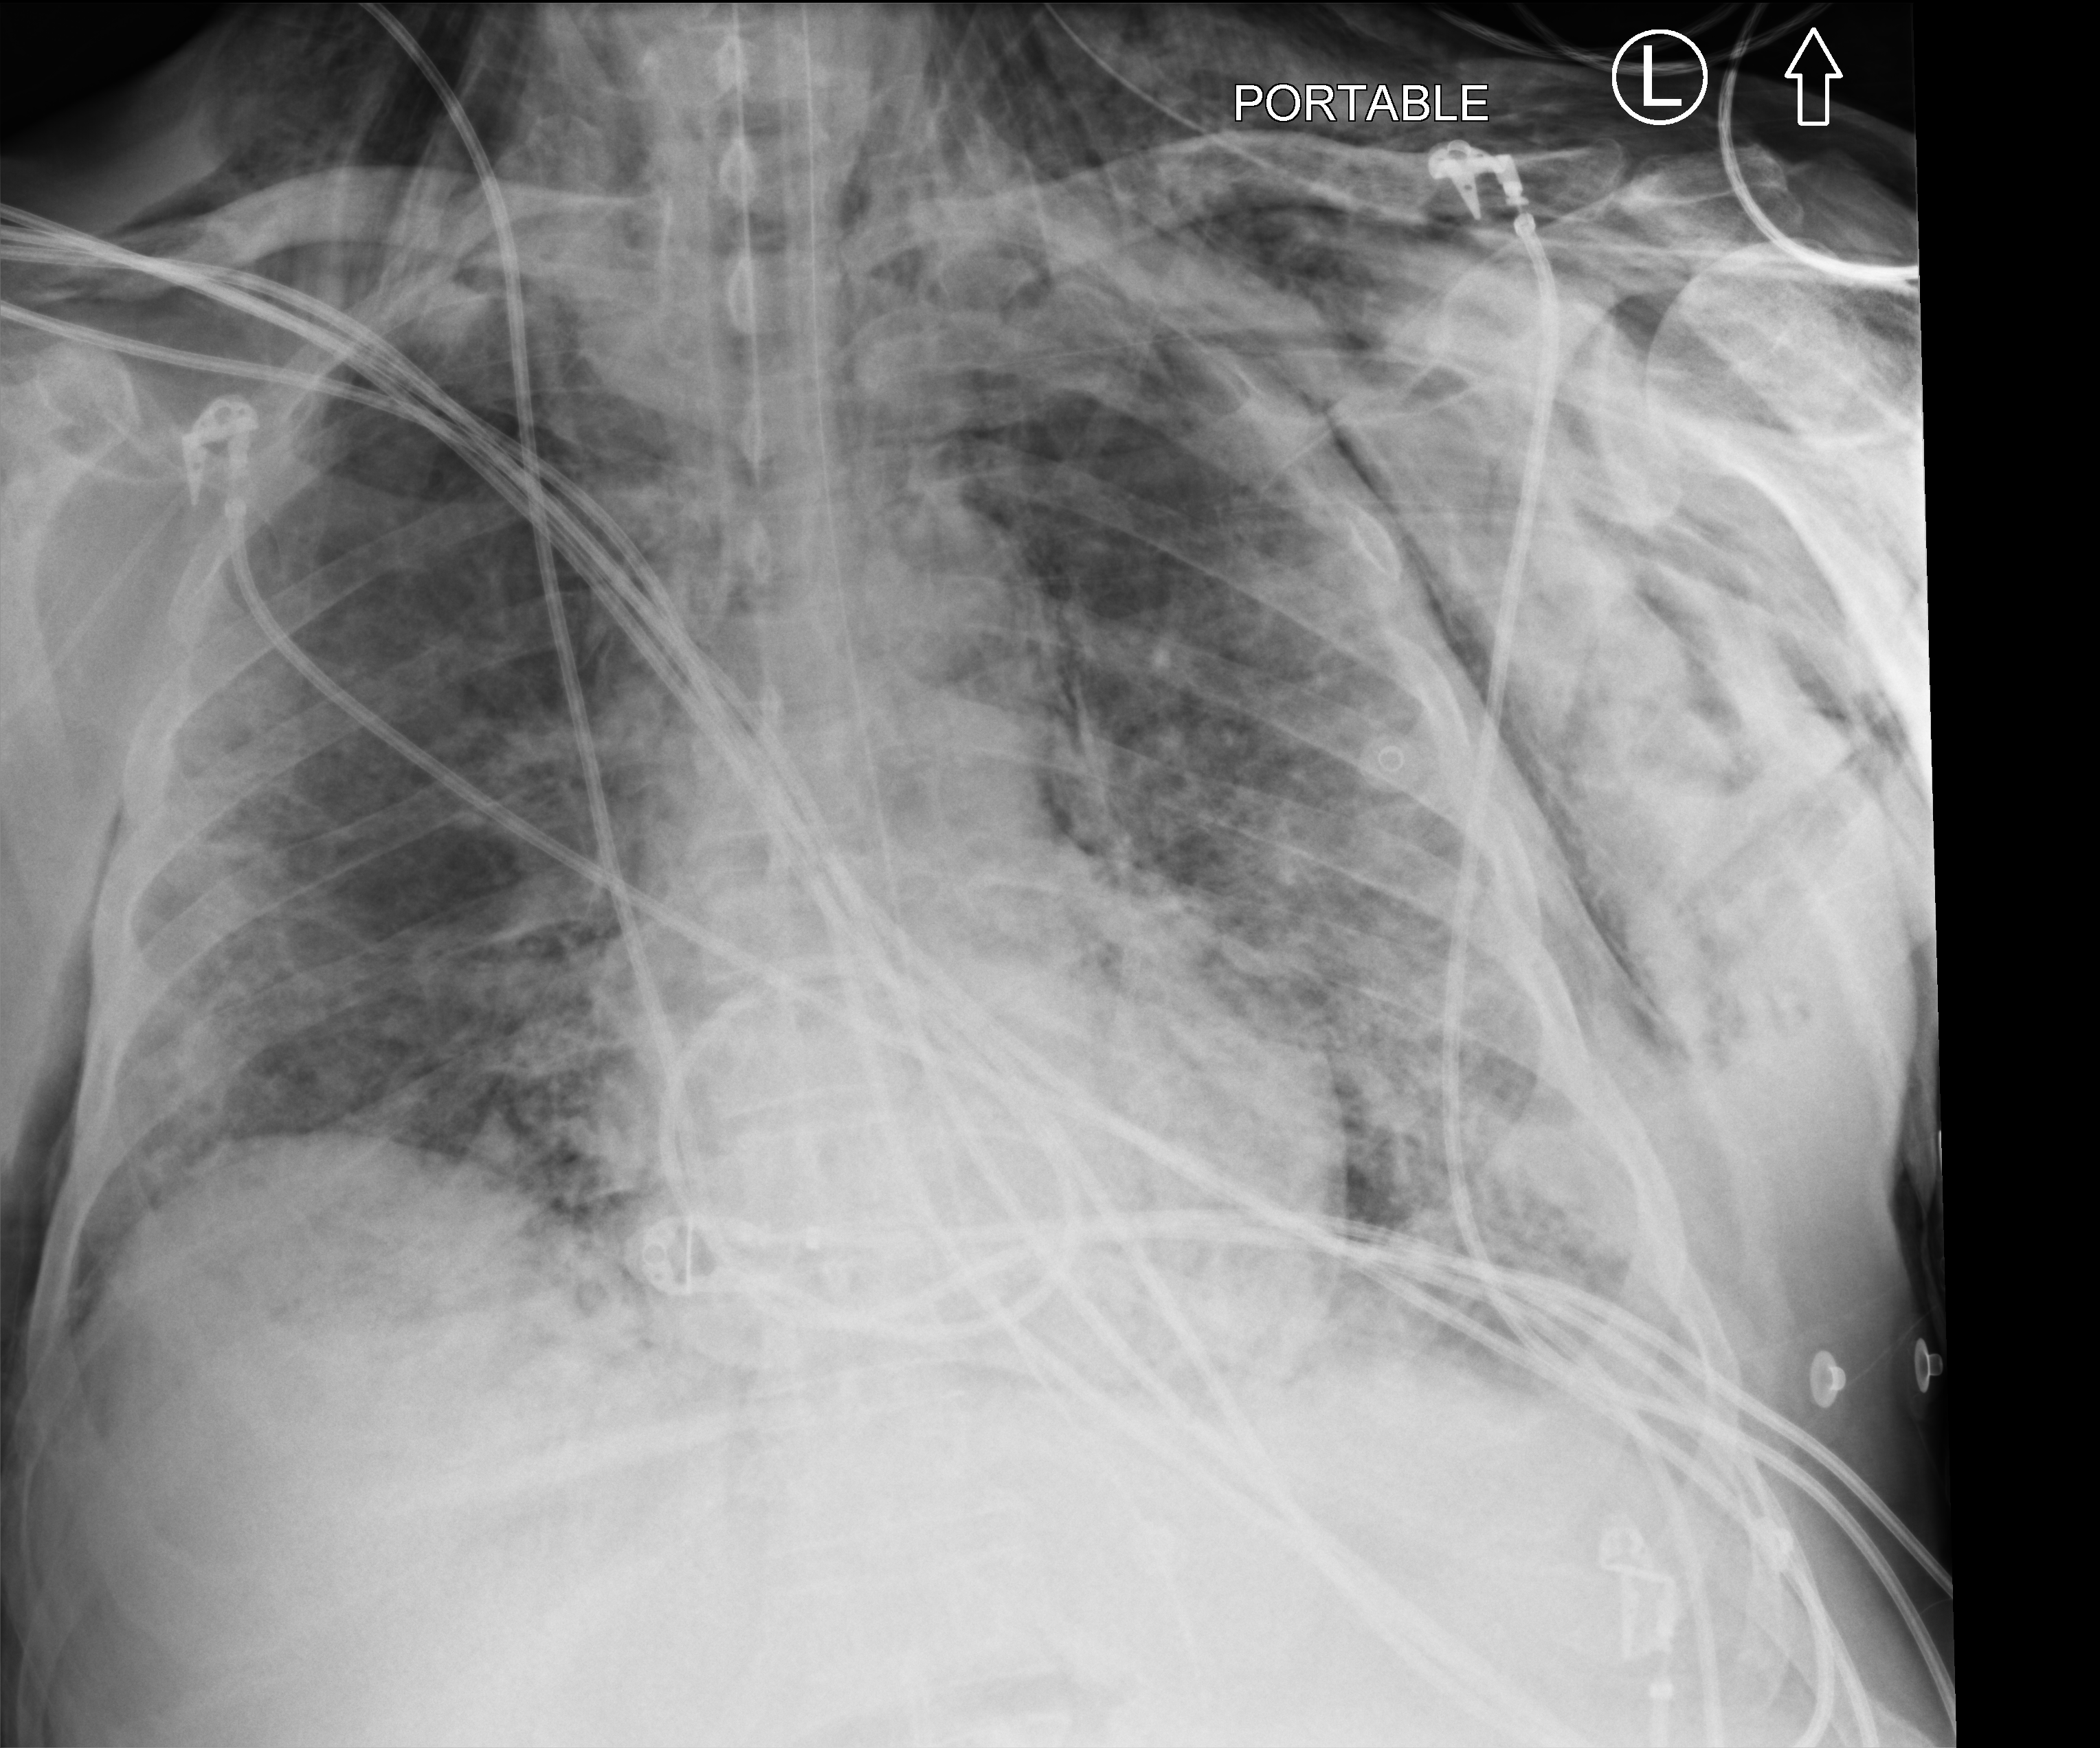
Portable chest radiograph; anteroposterior (AP) projection. Patient hospitalised with COVID-19; male, aged 60–74 years.
Hospital-stay facts (about this admission, not read from this image; timing relative to this image not recorded): length of hospital stay: 26 days.